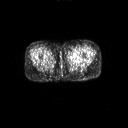
FDG PET of an extremity soft-tissue mass (from a PET/CT study), one axial slice; slice 7 of 267 in the series (ordered by position); 3.27 mm slice thickness; 128 × 128 image matrix. Patient: female, 47 years. Case-level facts recorded for this patient, not image findings: histological type: myxofibrosarcoma; grade: intermediate; site of the primary tumour: left thigh.
Annotated regions visible in this slice (expert contour drawn on MRI and transferred to this co-registered scan by the dataset authors):
- gross tumour volume including surrounding oedema: bounding box (x1, y1, x2, y2) in pixels: (68, 53, 81, 61)